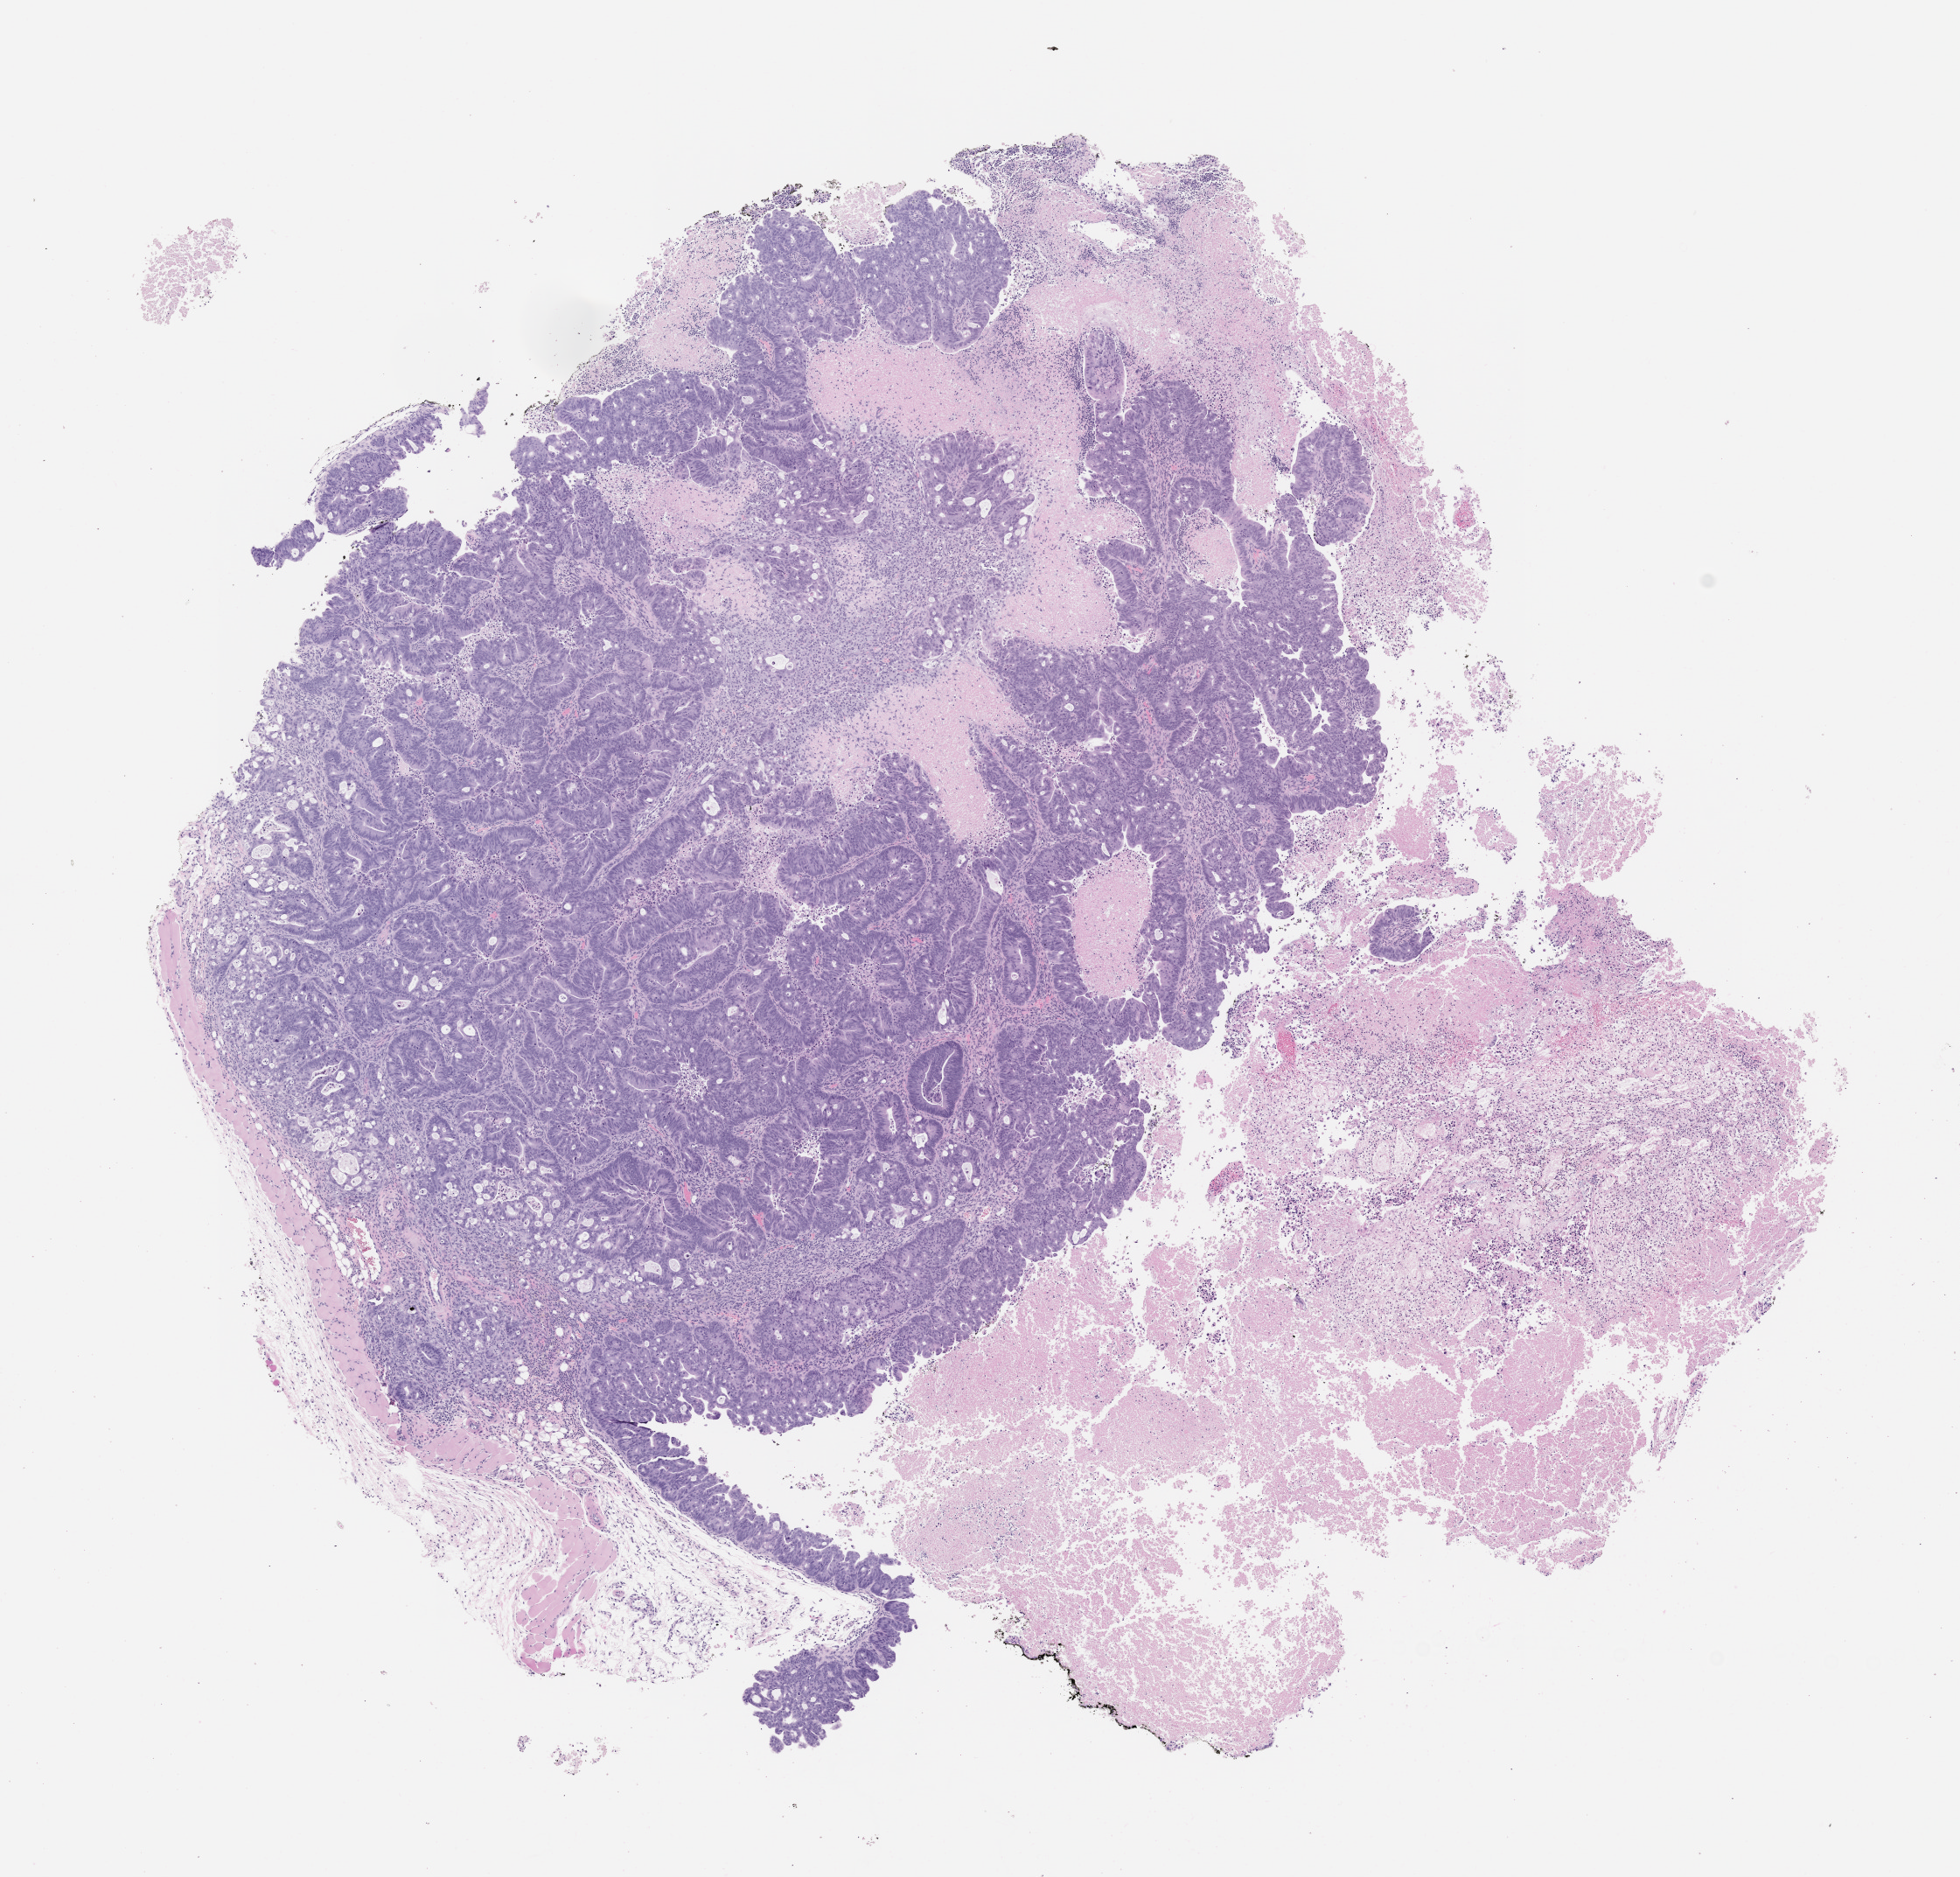
Whole-slide image, H&E: patient-derived xenograft (human tumor grown in a mouse), passage 1 — a low-resolution overview of the entire scanned area, about 9.0 x 8.6 mm, formalin-fixed, paraffin-embedded (FFPE) tissue, originating tumor site category: rectum.
Originating patient diagnosis: Rectal Adenocarcinoma.